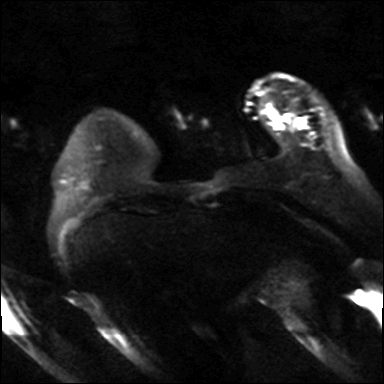
Breast MRI, one axial slice. Position 8 of 36 along the scan axis. Diffusion-weighted series; image 2 of 4 stored at this slice position (different b-values; order by instance number). 3 T. 4 mm slice thickness. 384 × 384 image matrix, field of view 320 × 320 mm. Female patient.
Outlined on this slice (outlined manually by an expert reader):
- tumour on diffusion-weighted imaging: bounding box (x1, y1, x2, y2) in pixels: (271, 111, 309, 128)